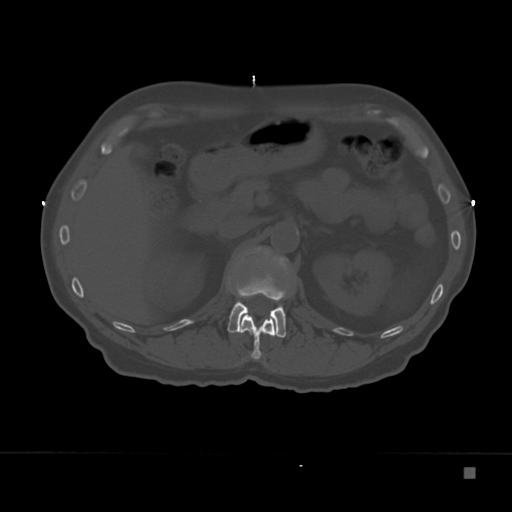
CT including the spine, one axial slice. Slice 119 of 332 in the series (ordered by position). 120 kVp. Bone window (W 1800 / L 400 HU). 1.5 mm slice thickness. 512 × 512 image matrix, field of view 389 × 389 mm. Male patient, age 72 years. From the clinical record (not read from this slice): primary cancer: skeletal.
Annotated regions visible in this slice (semi-automatic segmentation, software-assisted and operator-edited):
- L1 vertebra: bounding box <227,246,287,338> (left, top, right, bottom; pixels)
- T12 vertebra: <241,314,275,360>